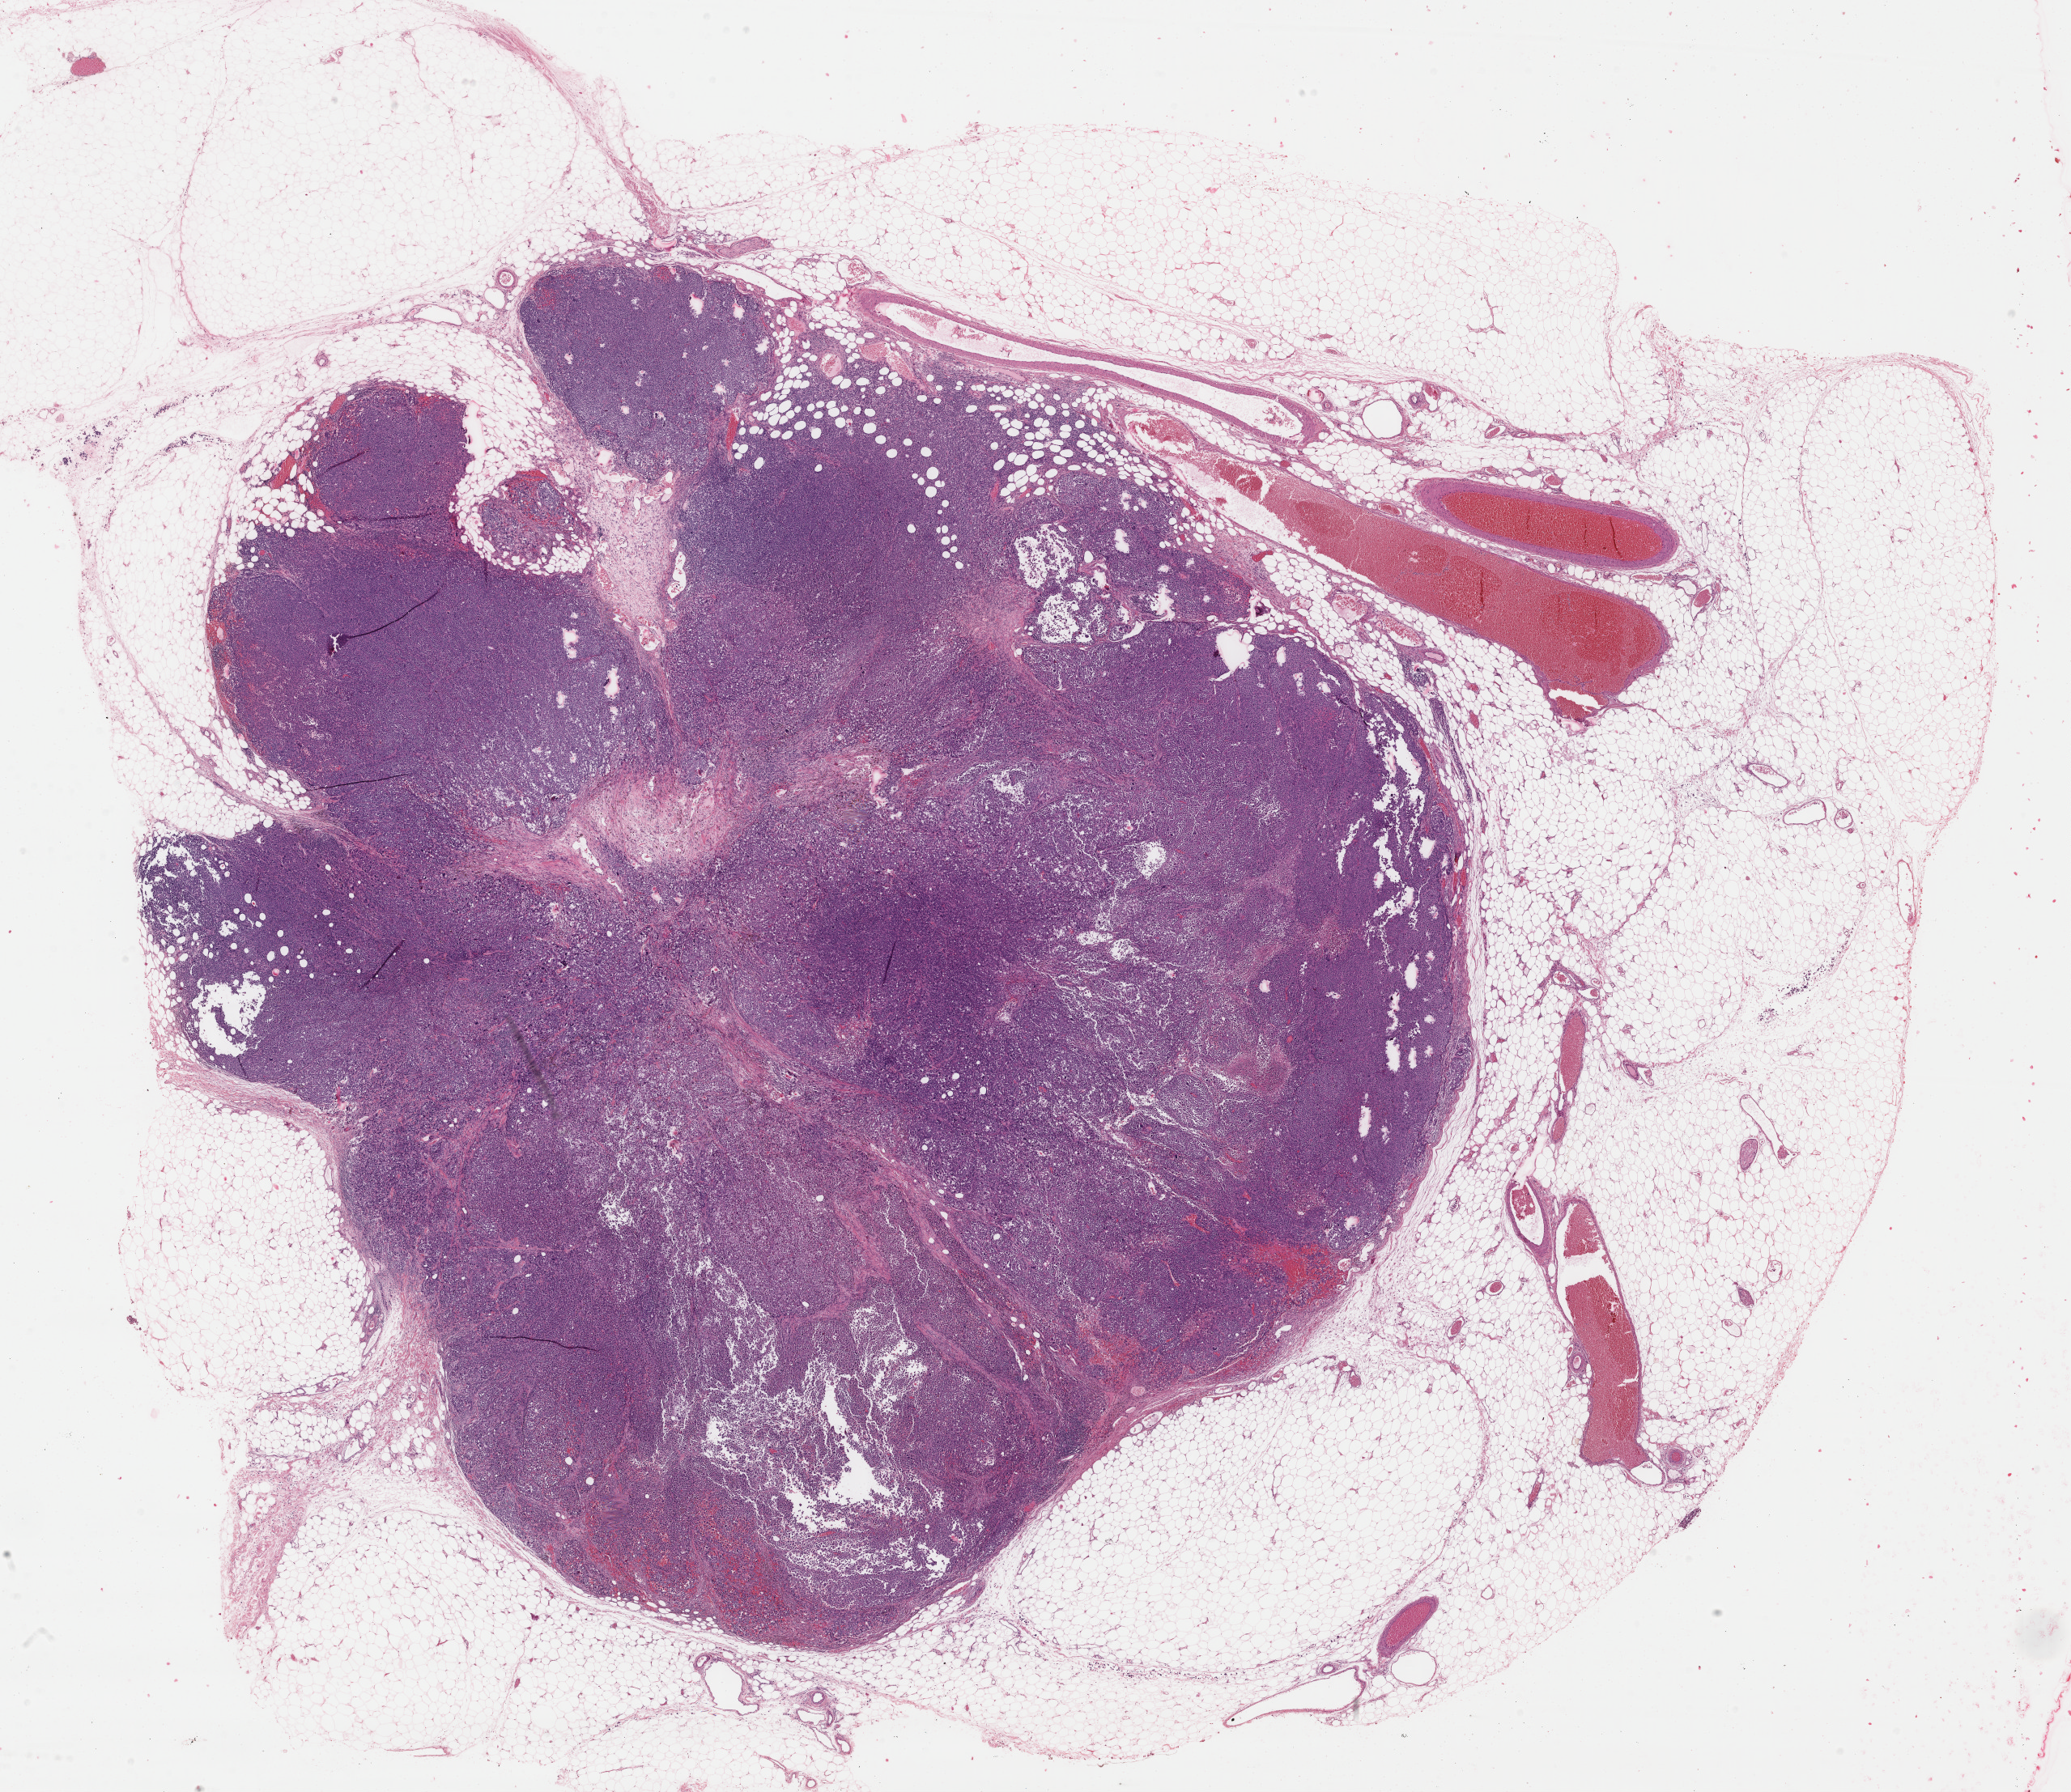
Whole-slide histology image, H&E-stained, low-resolution overview of the scanned area, about 20.3 x 17.6 mm (slide scanned at 40x); FFPE section; sample: primary tumour, skin. Patient: male, age at initial diagnosis 80 years.
* histologic diagnosis: Malignant melanoma, NOS